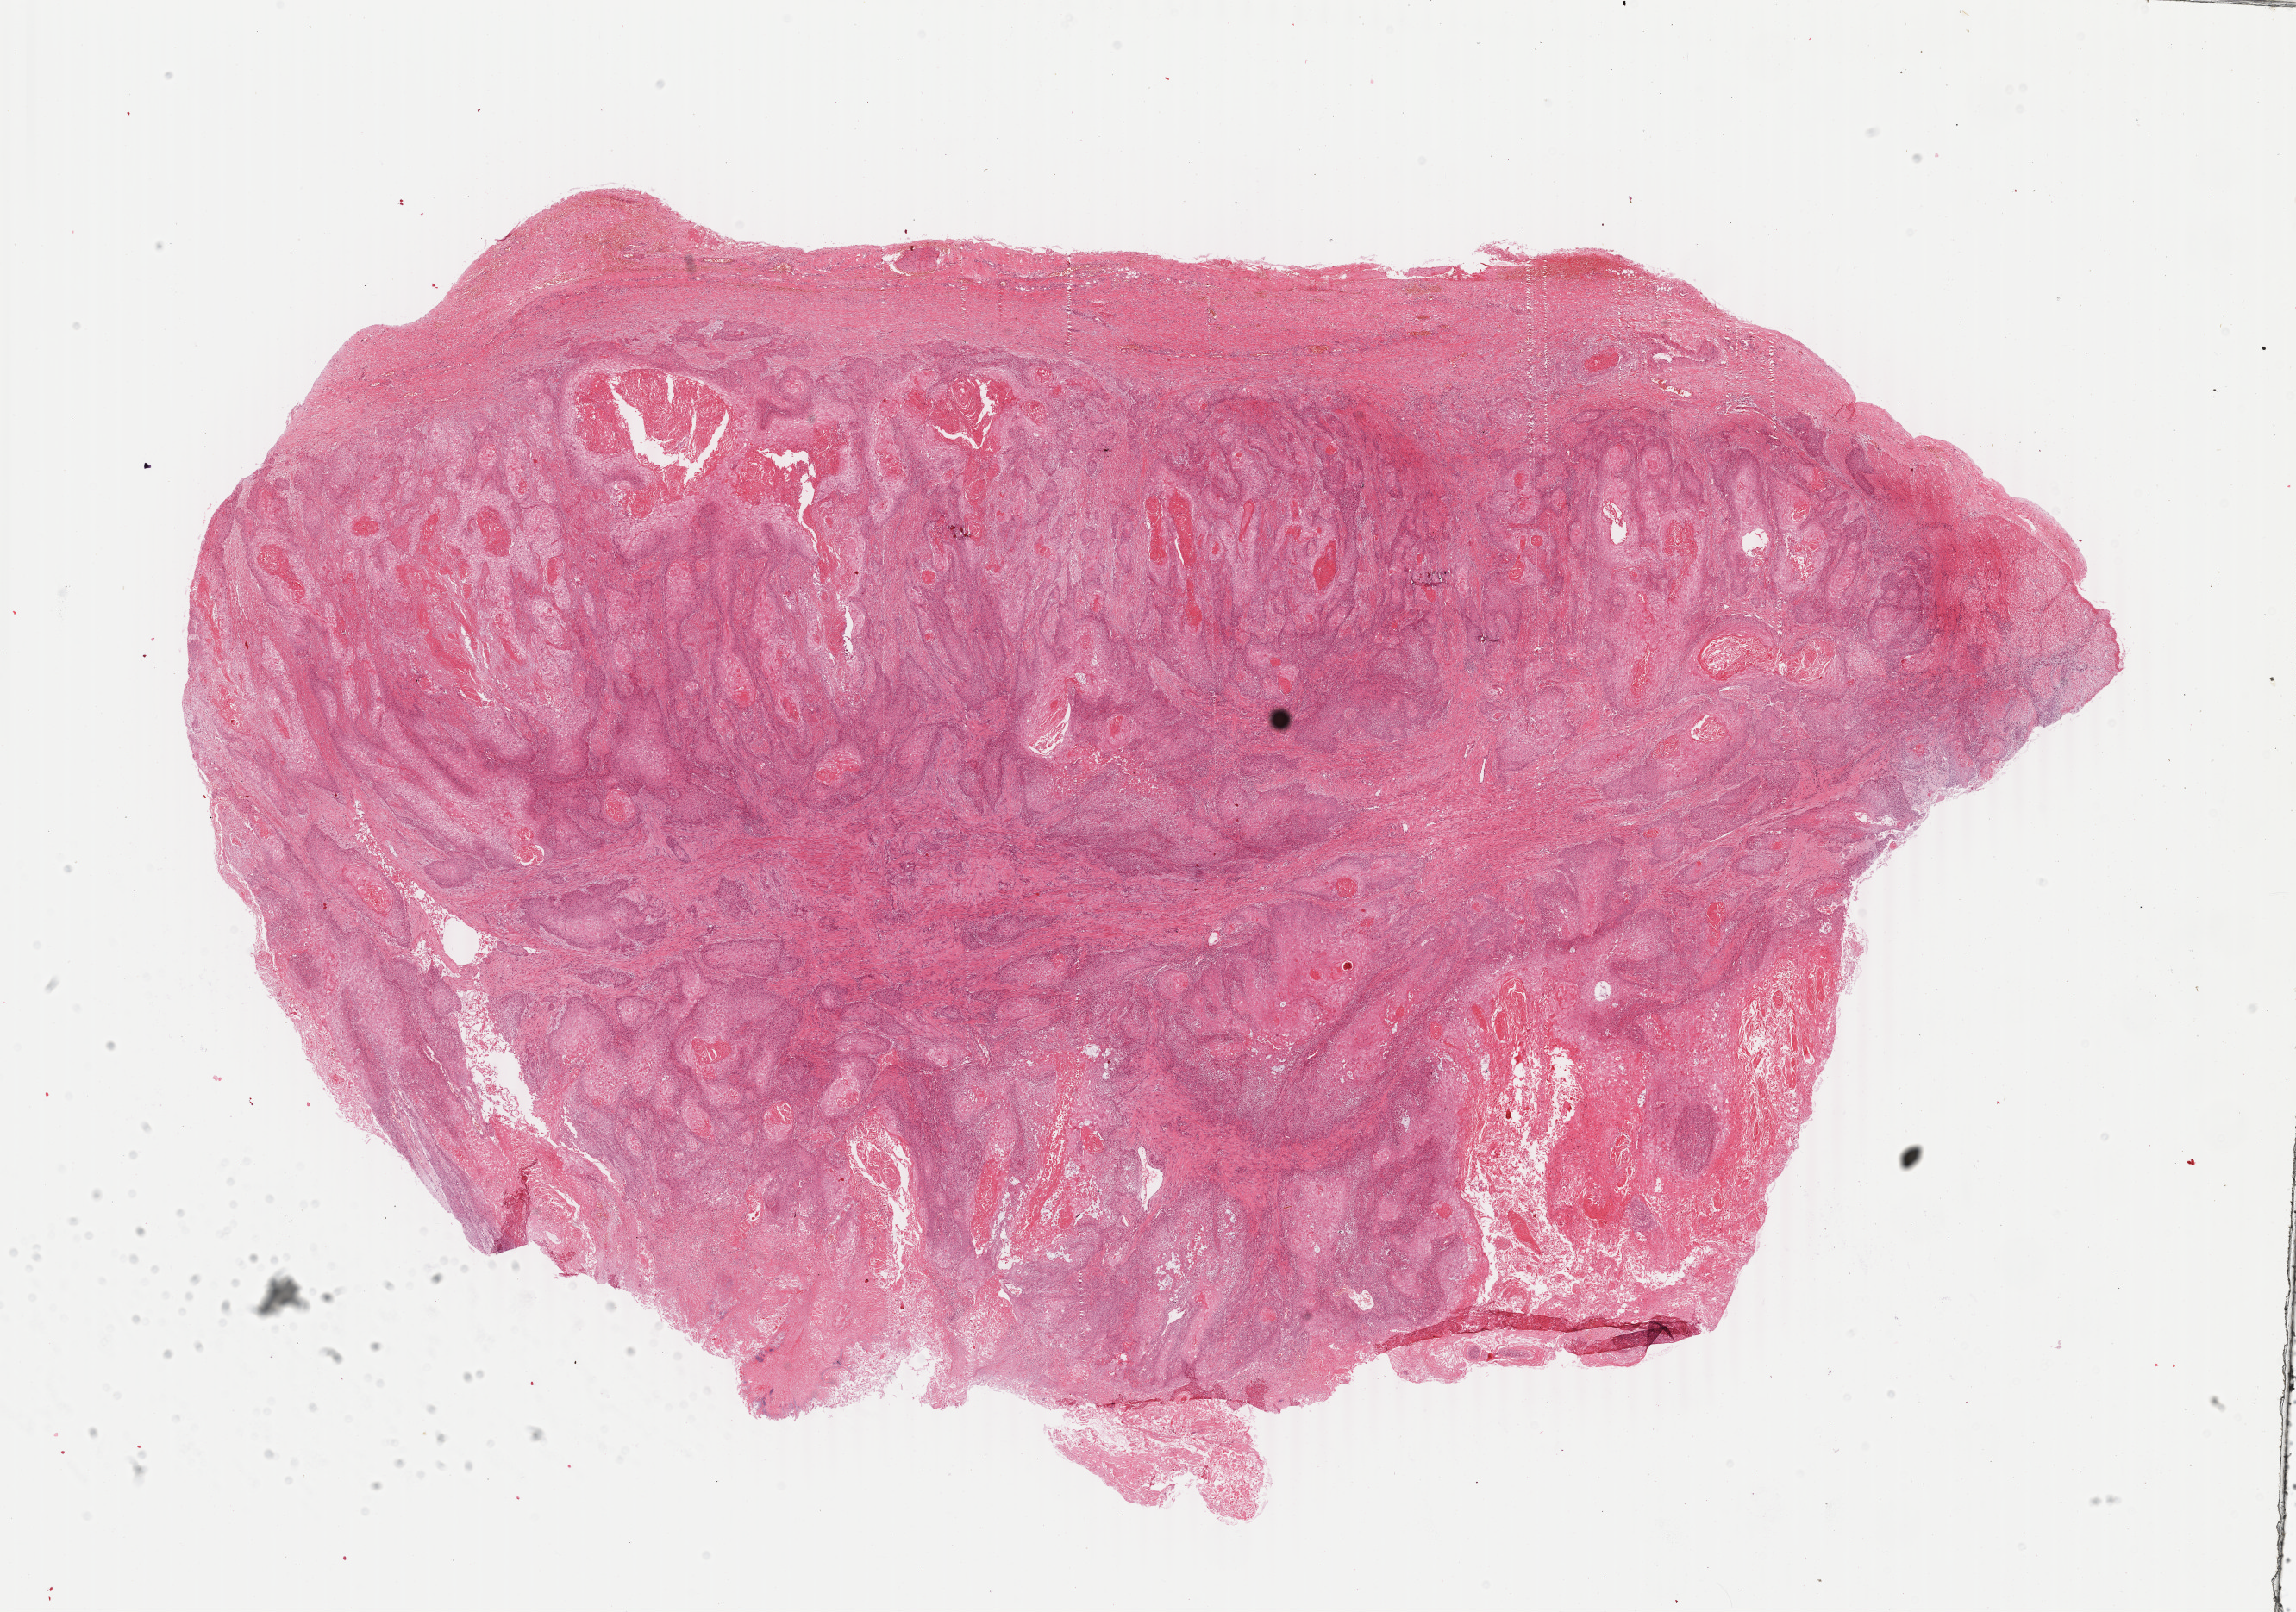
Hematoxylin and eosin (H&E) stained whole-slide image — low-resolution overview of the scanned area, about 21.2 x 14.9 mm (from a 40x scan), FFPE section, primary tumour sample from the esophagus. Patient: male, age at initial diagnosis 62 years. Histologic grade: G1 (well differentiated).
AJCC pathologic stage: IIA. Diagnosis: Squamous cell carcinoma, NOS (lower third of esophagus).